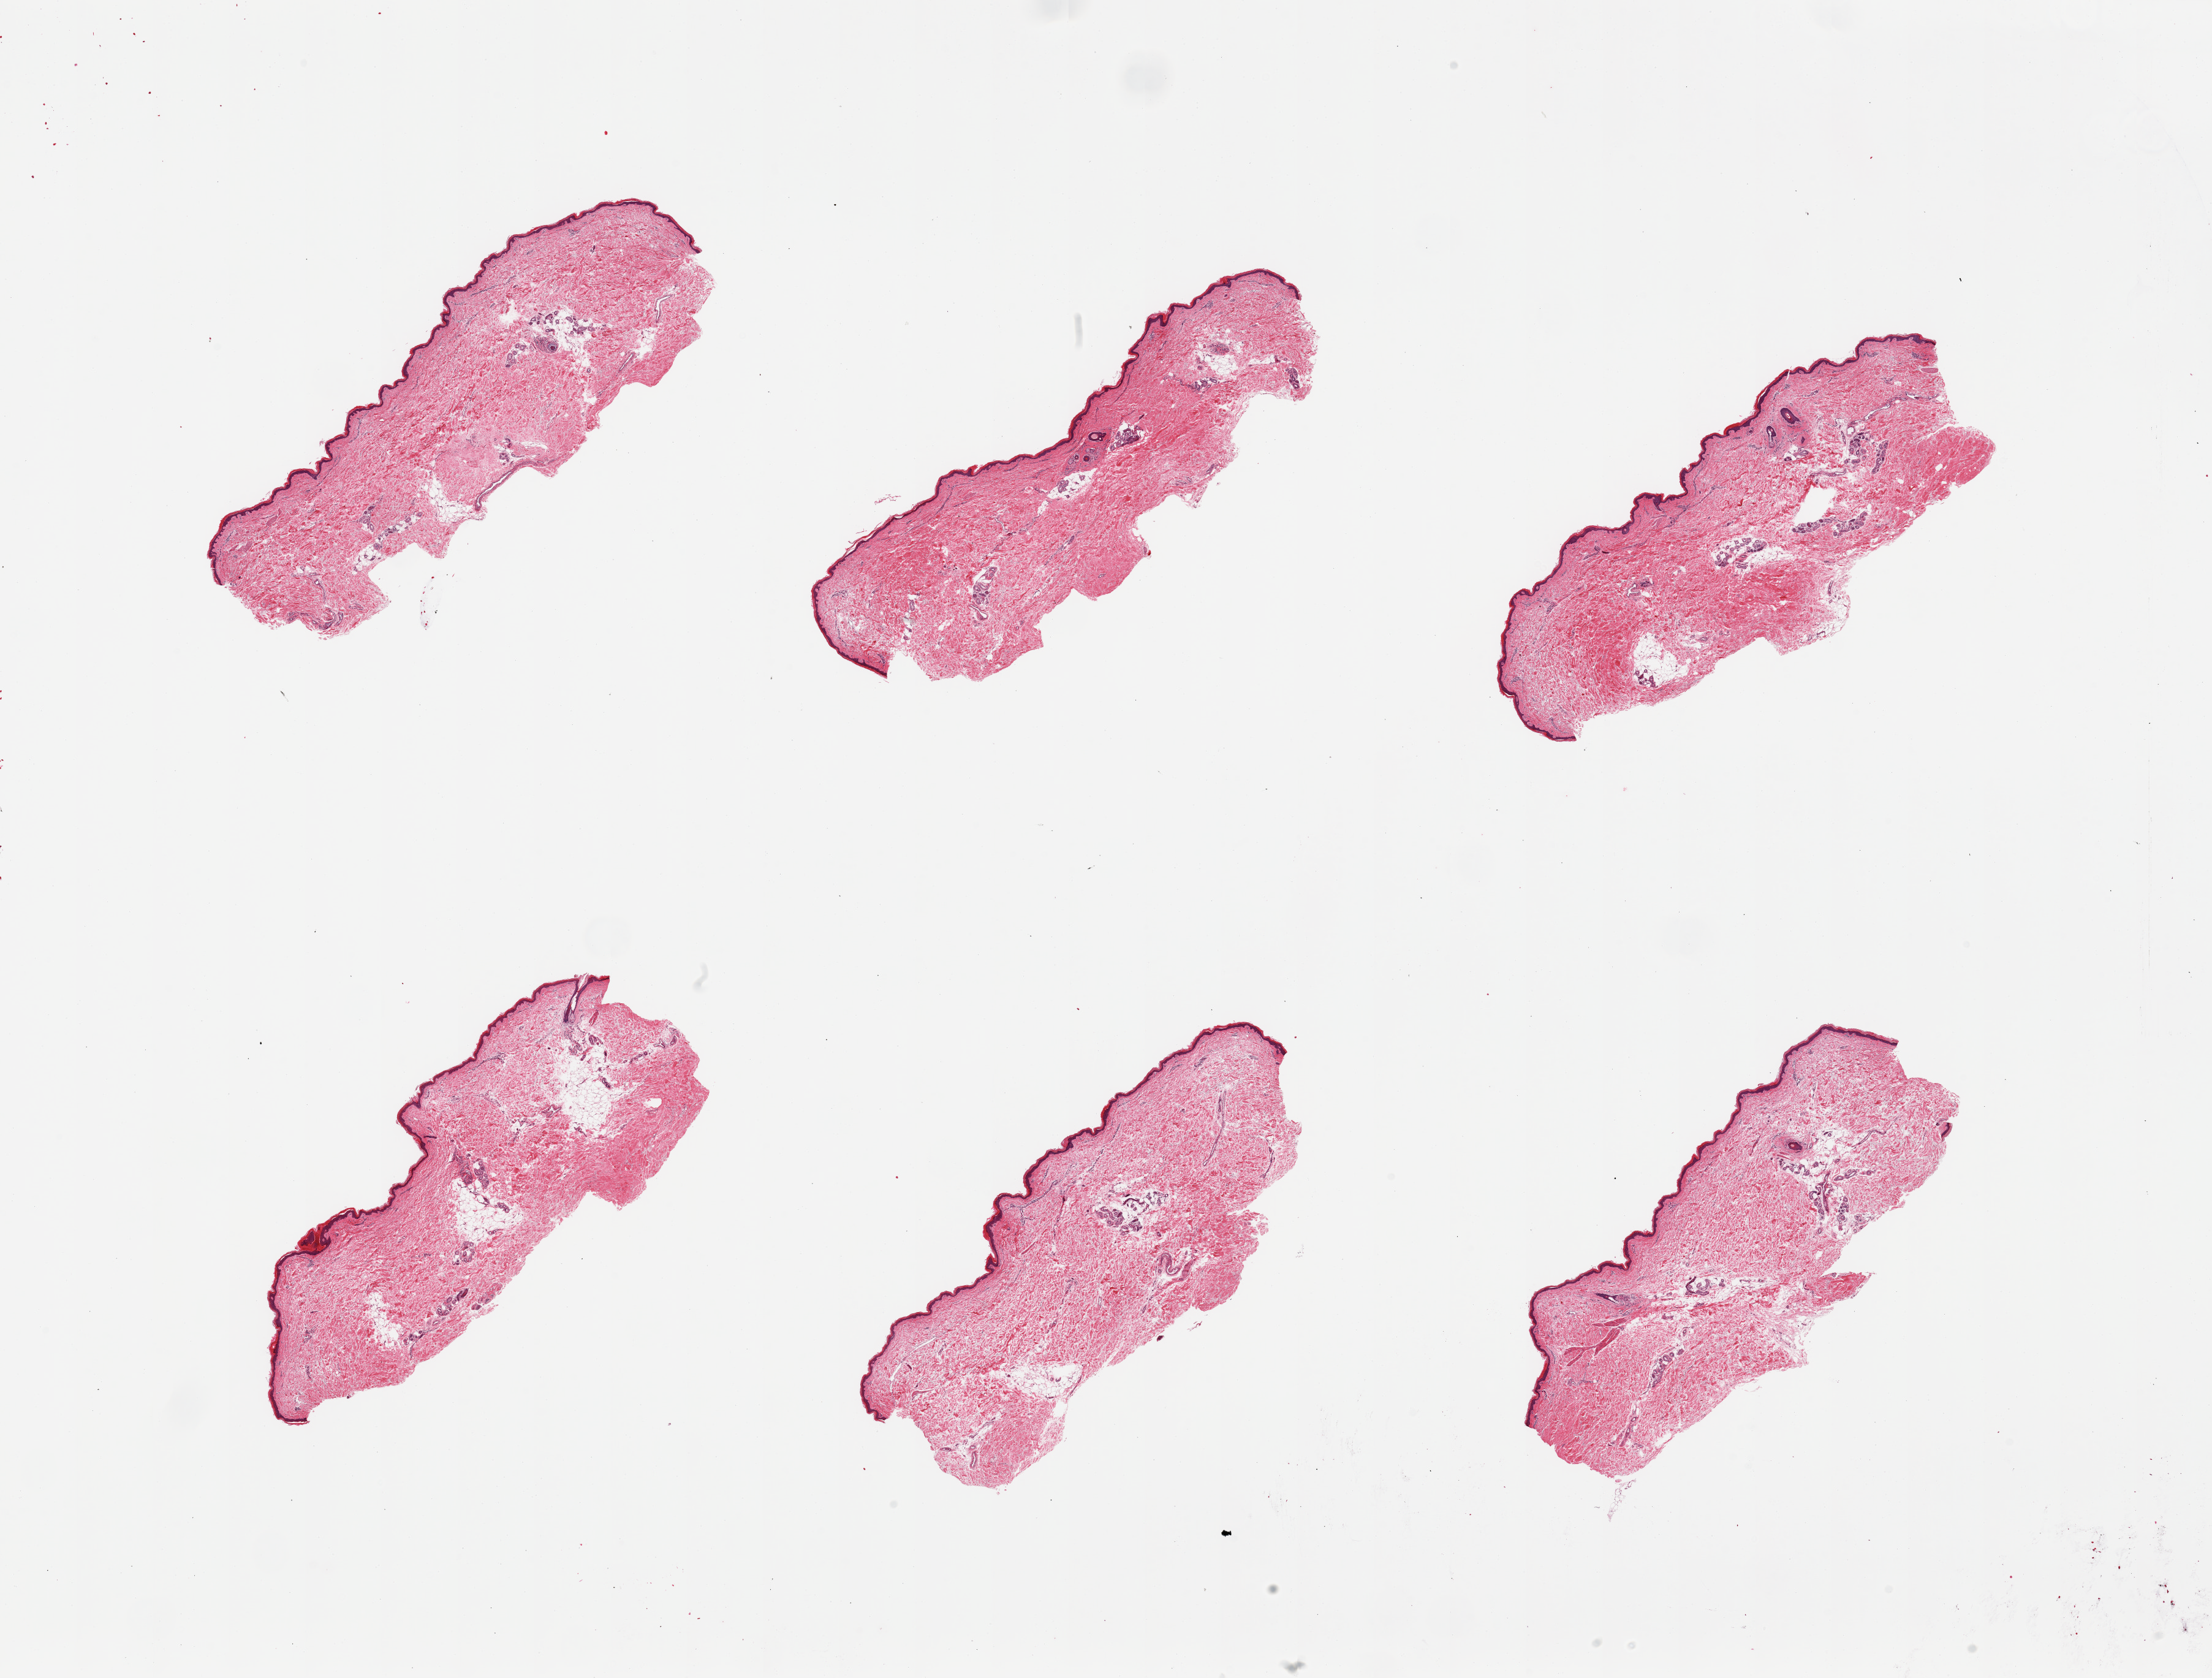
Whole-slide image, hematoxylin and eosin (H&E) stain, a low-resolution overview of the entire scanned area, about 28.5 x 21.7 mm (acquisition: 20x scan); PAXgene-fixed, paraffin-embedded tissue; sampled site (target tissue): skin of lower leg; tissue donor sample. Donor: male.
Review note (as recorded): 6 pieces; ~10% internal (periadnexal) fat; epidermis is 34um thick.